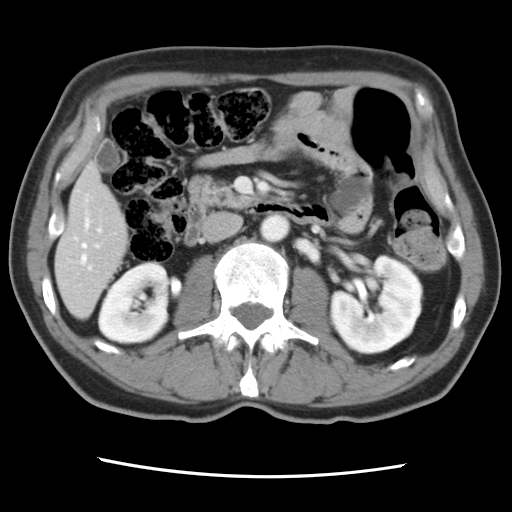
Contrast-enhanced abdominal CT, one axial slice; slice 30 of 83 in the series (ordered by position); intravenous contrast given; soft-tissue window (W 400 / L 40 HU); 5 mm slice thickness; 512 × 512 image matrix, field of view 321 × 321 mm. Male patient, age 69 years. From the clinical record (not read from this slice): diagnosis: colorectal cancer liver metastases, imaged before liver resection; multiple liver metastases: yes; largest metastasis: 3.5 cm.
Annotated regions visible in this slice (manually delineated by an expert):
- hepatic veins: box from (x=75, y=219) to (x=99, y=262) px
- liver: (x=56, y=167)–(x=128, y=317)
- planned liver remnant (the part of the liver to remain after resection): (x=56, y=166)–(x=128, y=317)
- portal vein (with intrahepatic branches): (x=89, y=229)–(x=102, y=269)